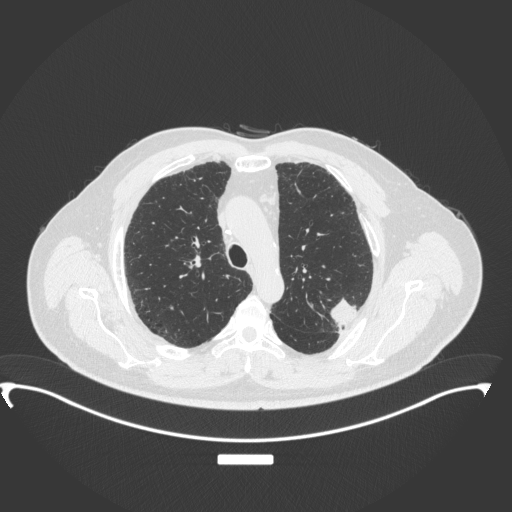
Chest CT, one axial slice. Position 262 of 350 along the scan axis. Reconstruction kernel B31f. 120 kVp. Lung window (W 1500 / L -600 HU). 1 mm slice thickness. 512 × 512 image matrix, field of view 459 × 459 mm. Patient: male, 64 years. Case-level facts recorded for this patient, not image findings: clinical TNM (as recorded): T1c N1 M1.
Annotated regions visible in this slice (bounding box drawn by a radiologist):
- lung tumour (recorded histology: adenocarcinoma): bounding box [x1, y1, x2, y2] px = [325, 294, 363, 330]